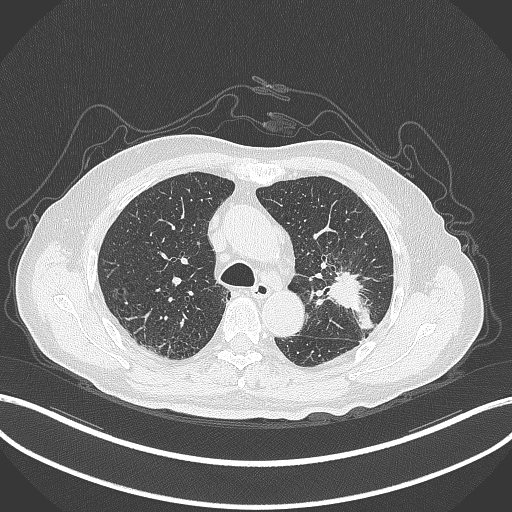
Chest CT, one axial slice. Position 198 of 331 along the scan axis. Reconstruction kernel B70f. Lung window (W 1500 / L -600 HU). 1 mm slice thickness. 512 × 512 image matrix, field of view 400 × 400 mm. Male patient, age 79 years. From the clinical record (not read from this slice): clinical TNM (as recorded): T2a N1 M1; histopathological grade: G3.
Outlined on this slice (bounding box drawn by a radiologist):
- lung tumour (recorded histology: adenocarcinoma): bounding box <323,269,375,334> (left, top, right, bottom; pixels)